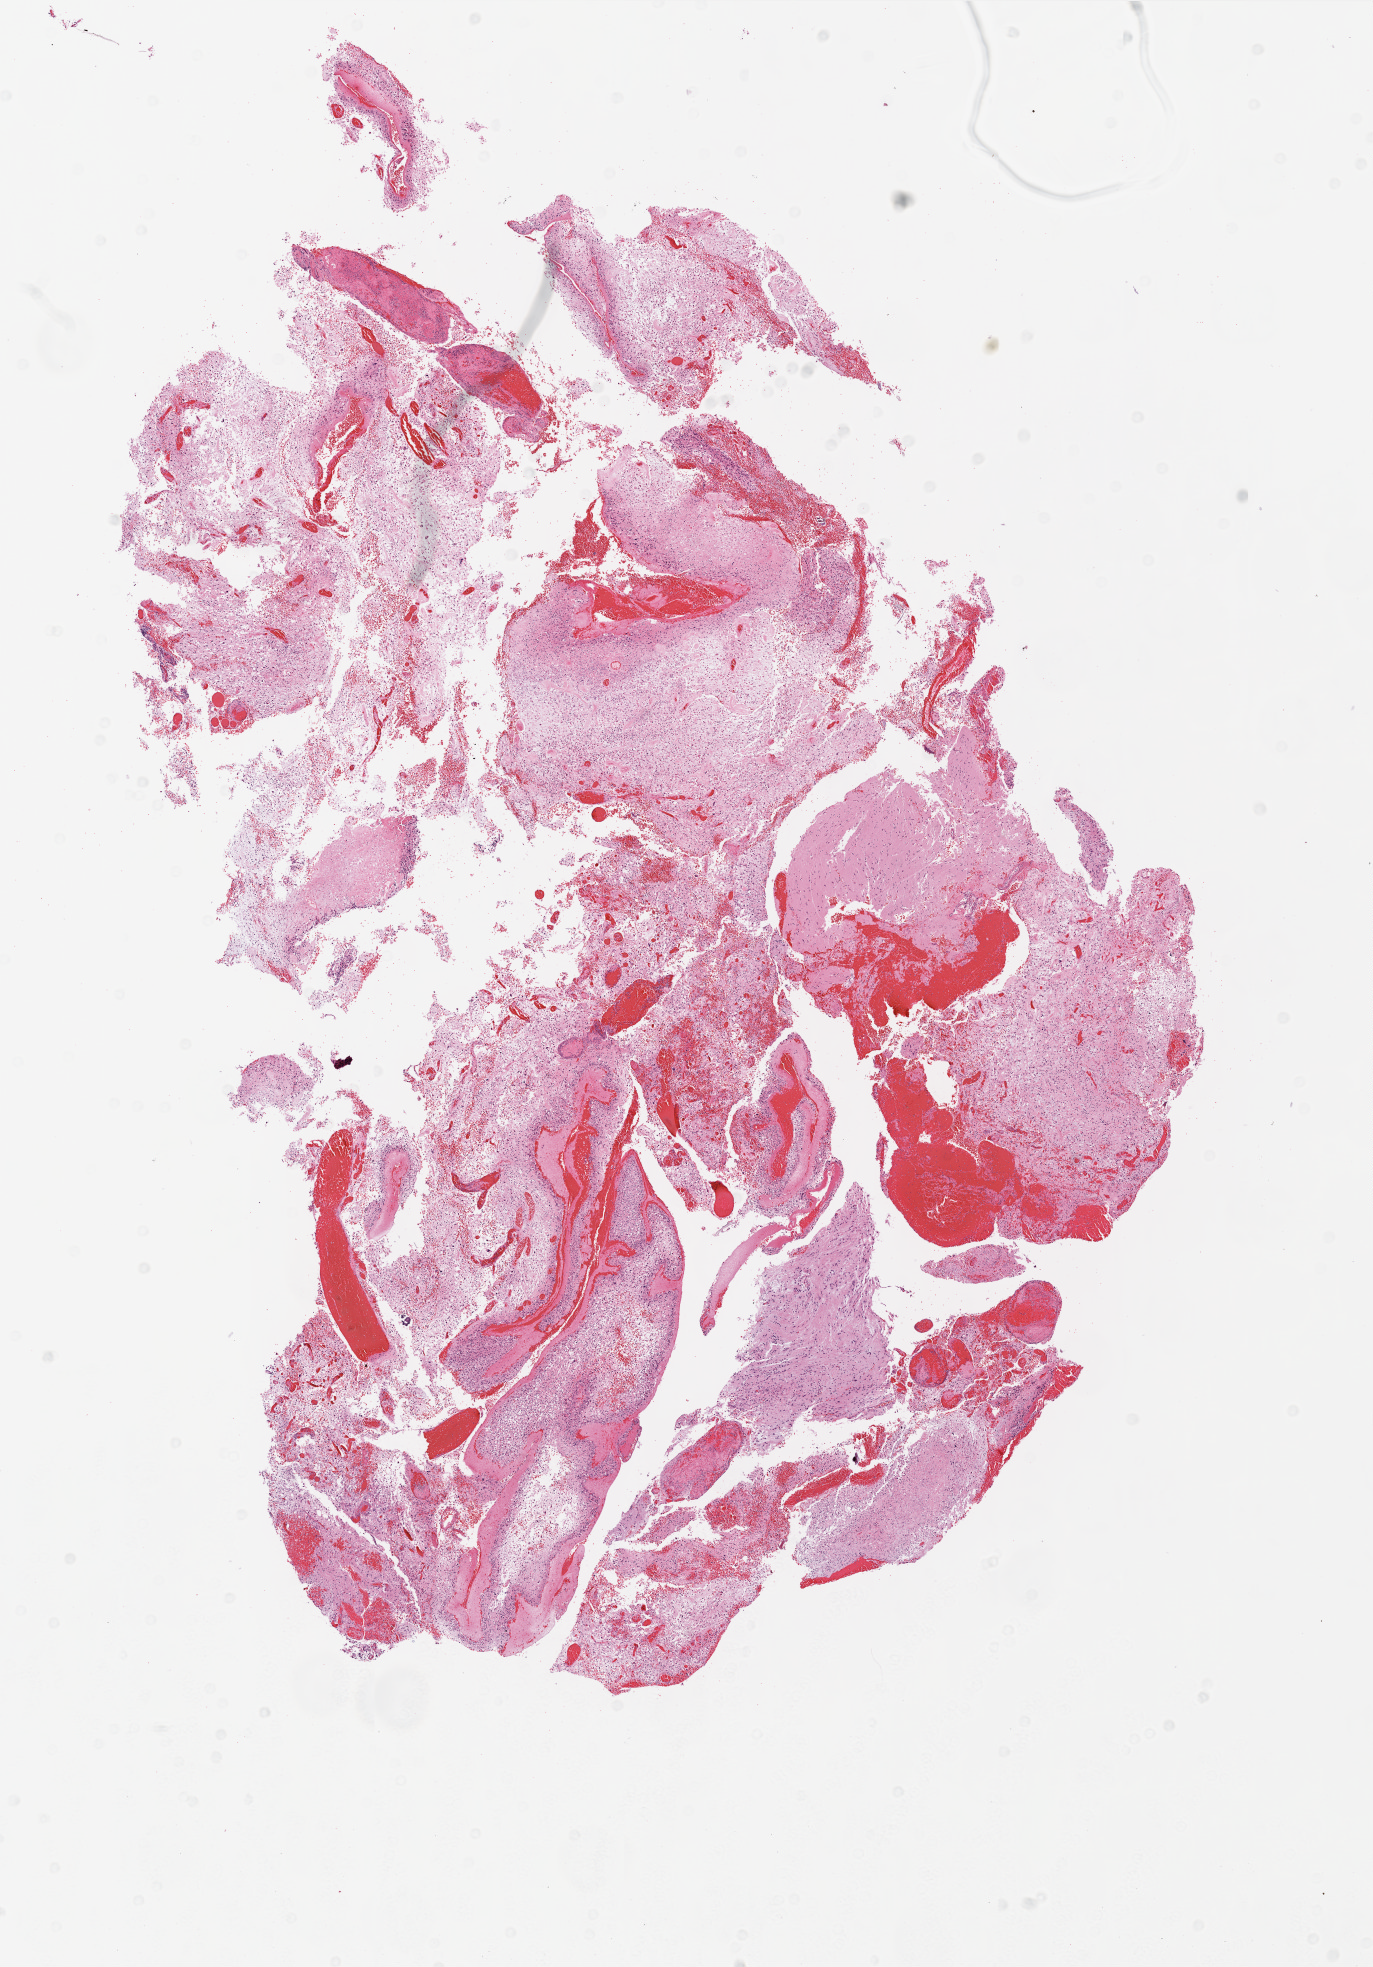
Hematoxylin and eosin (H&E) stained whole-slide image, a low-resolution overview of the entire scanned area, about 11.0 x 15.7 mm (acquisition: 20x scan); formalin-fixed paraffin-embedded (FFPE) diagnostic section; brain, primary tumour sample. Patient: female, age at initial diagnosis 65 years.
Diagnosis: Glioblastoma.